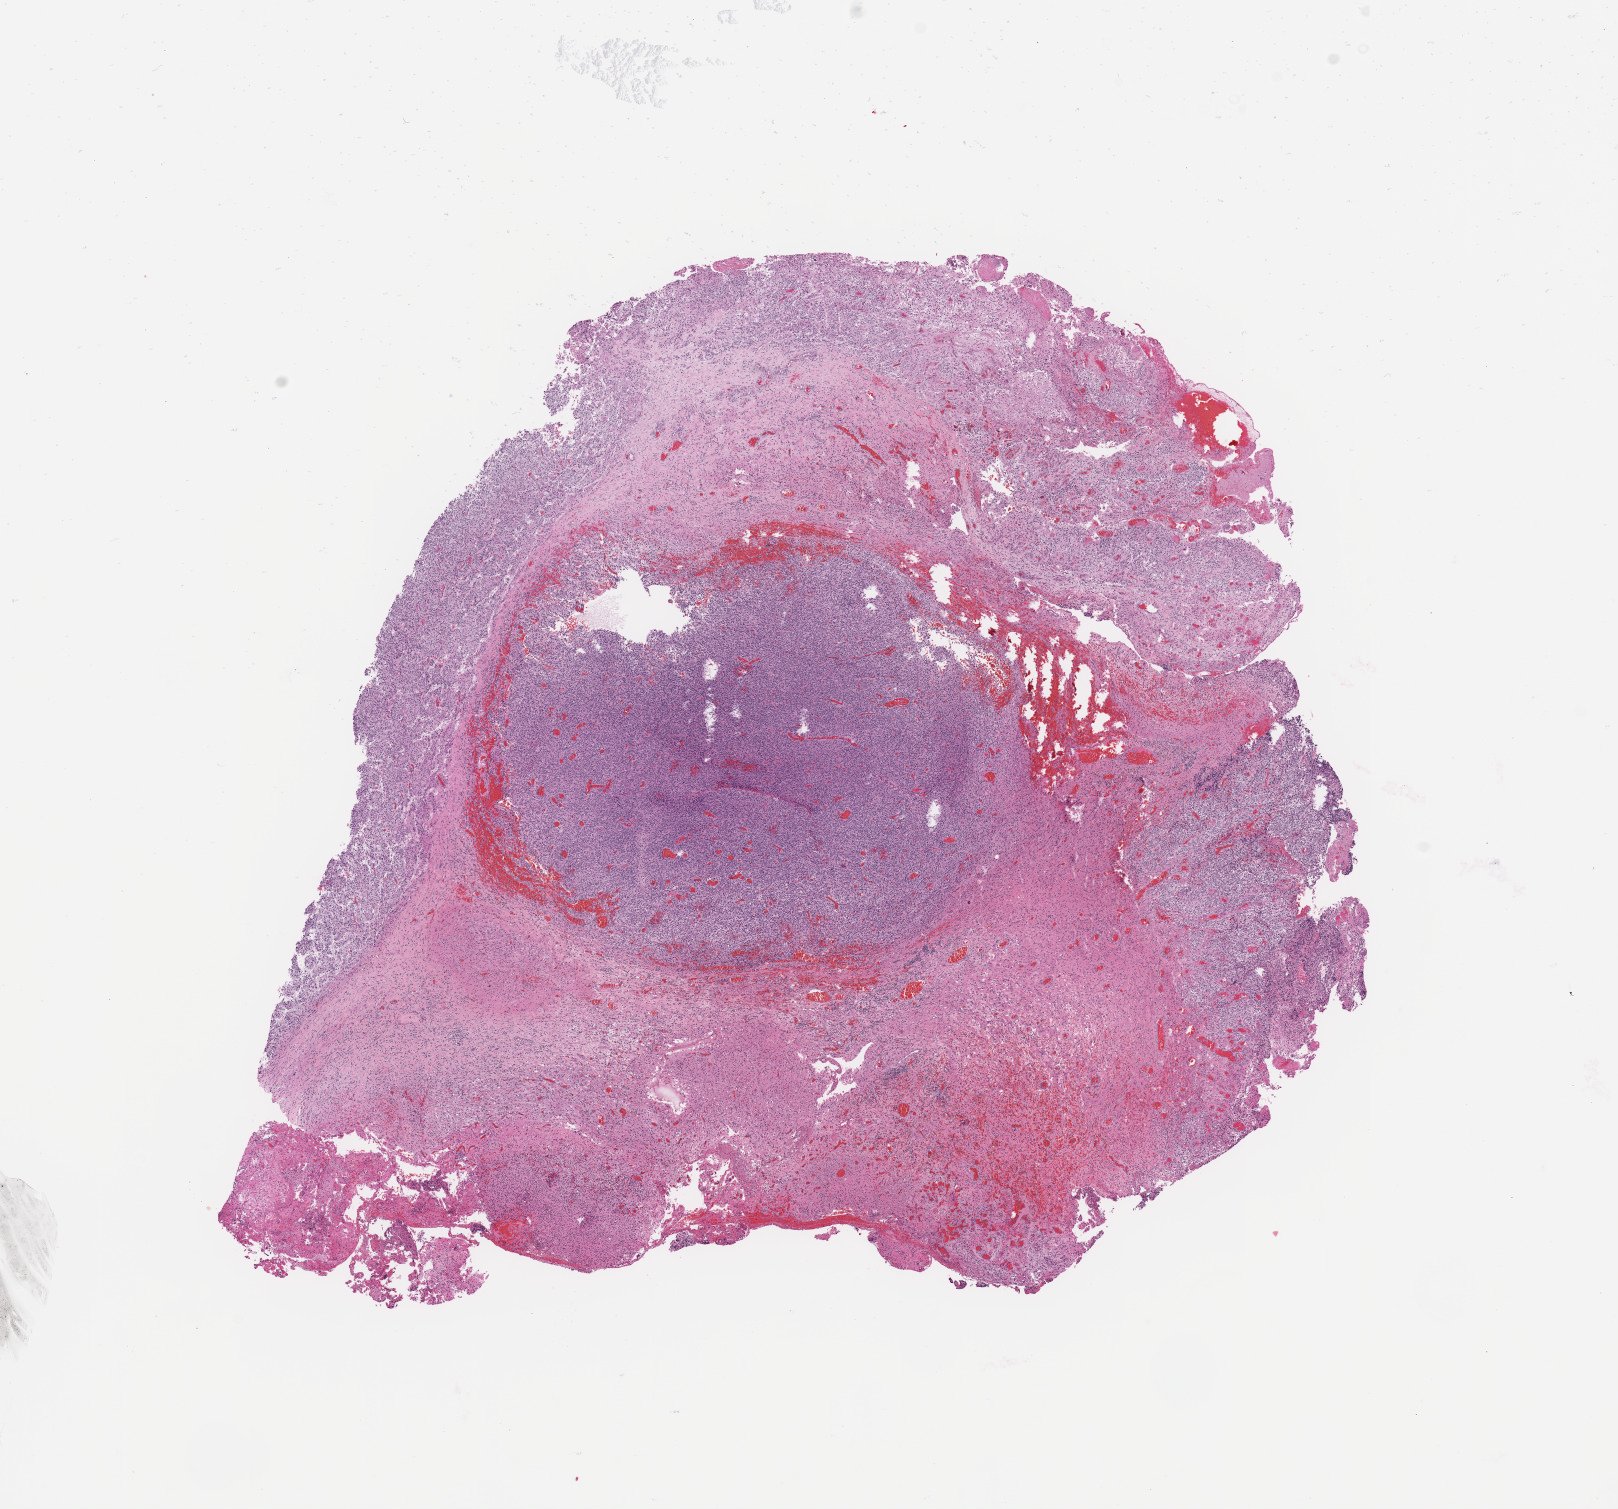
Digitized H&E-stained tissue section (whole slide), low-resolution overview of the scanned area, about 12.8 x 11.9 mm. Brain, tumour tissue. 59-year-old male patient.
Histologic diagnosis: Glioblastoma.